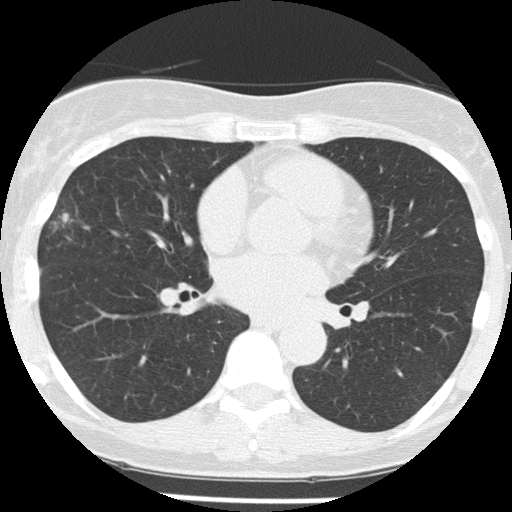
Axial slice from a low-dose chest CT screening exam. Baseline annual screen. Lung window (W 1500 / L -600 HU). Slice 77 of 156 in the series. Female participant, aged 58 years at enrolment. Former smoker at enrolment.
Expert-annotated lung lesion, bounding box (x1, y1, x2, y2) in pixels: (31, 194, 84, 253). Screening reader's record for this exam (one nodule recorded; not confirmed to be the boxed lesion): non-calcified nodule or mass ≥4 mm, right middle lobe, 18 × 9 mm, spiculated (stellate) margins, soft tissue attenuation. Participant outcome: lung cancer diagnosed 79 days after this screen — non-small cell carcinoma, right middle lobe, poorly differentiated (G3), stage IA (AJCC 6th edition), 18 mm at pathology.